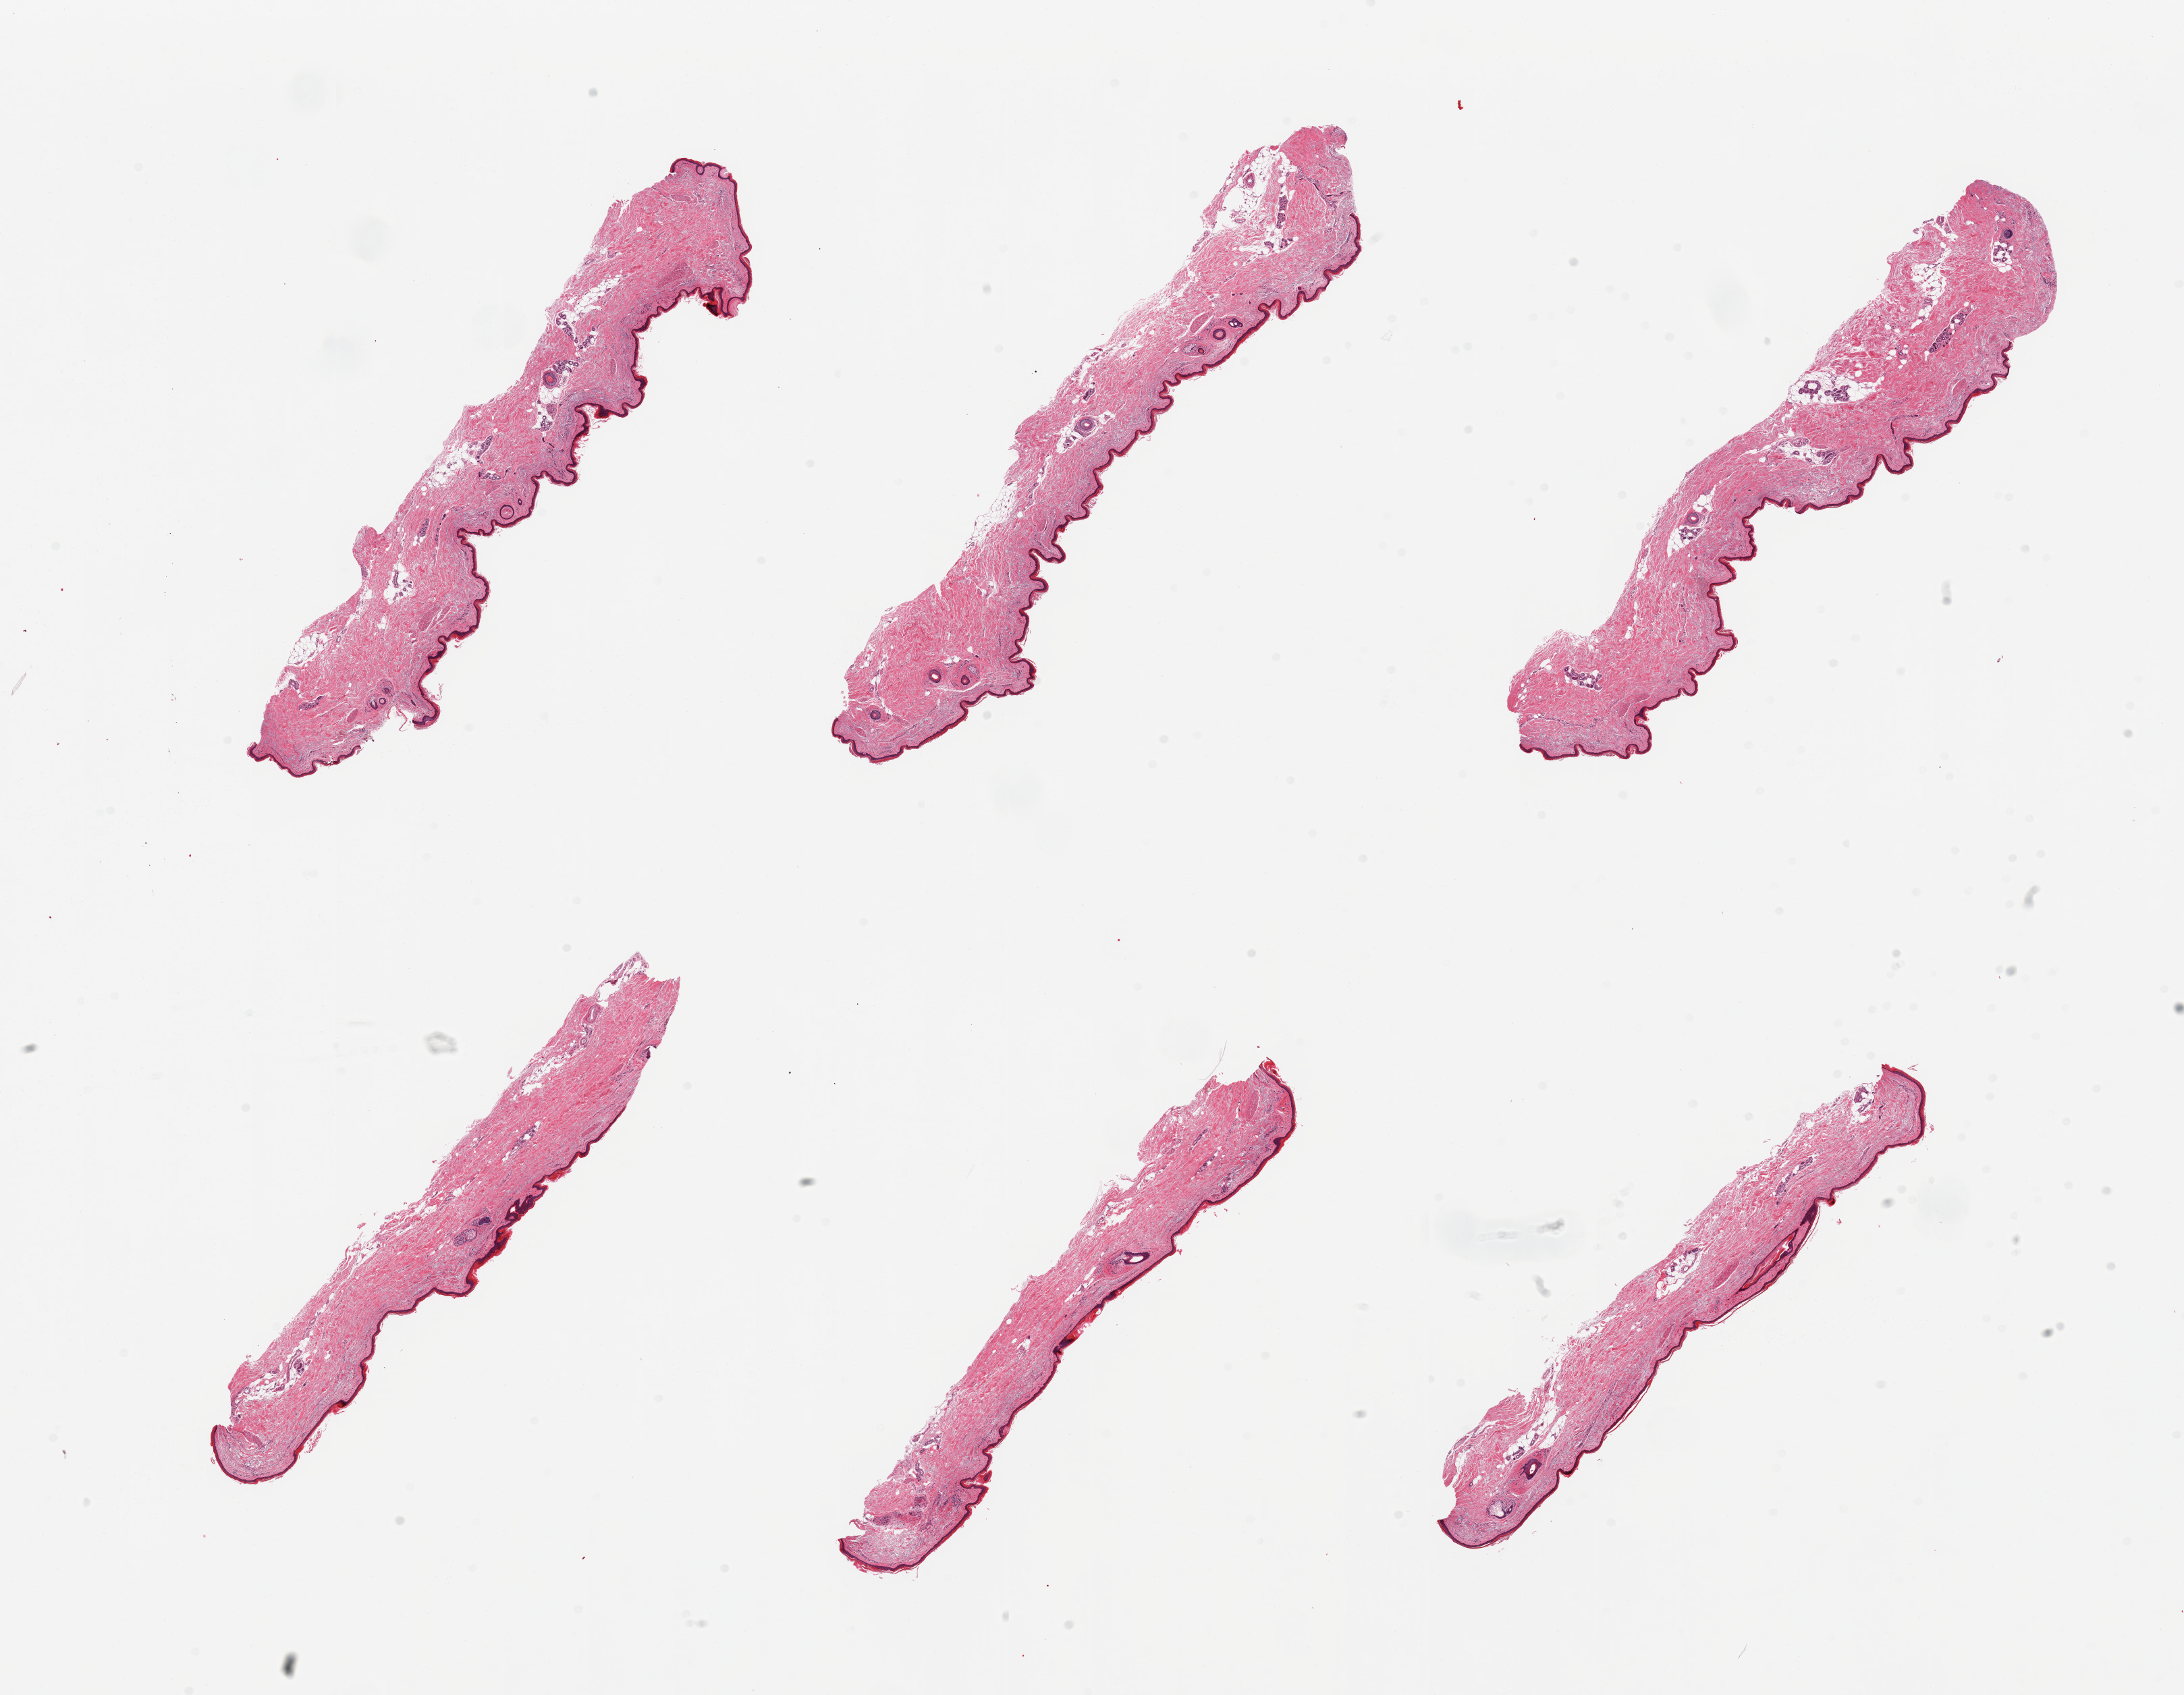
Haematoxylin and eosin whole-slide image — a low-resolution overview of the entire scanned area, about 25.6 x 19.9 mm. PAXgene-fixed paraffin-embedded (PFPE) section. Section of skin of lower leg (target tissue). Tissue donor sample. Donor: male.
Reviewer comment on this tissue sample: 6 pieces; attenuated epidermis (25um), solar elastosis; well trimmed, 10% dermal fat.